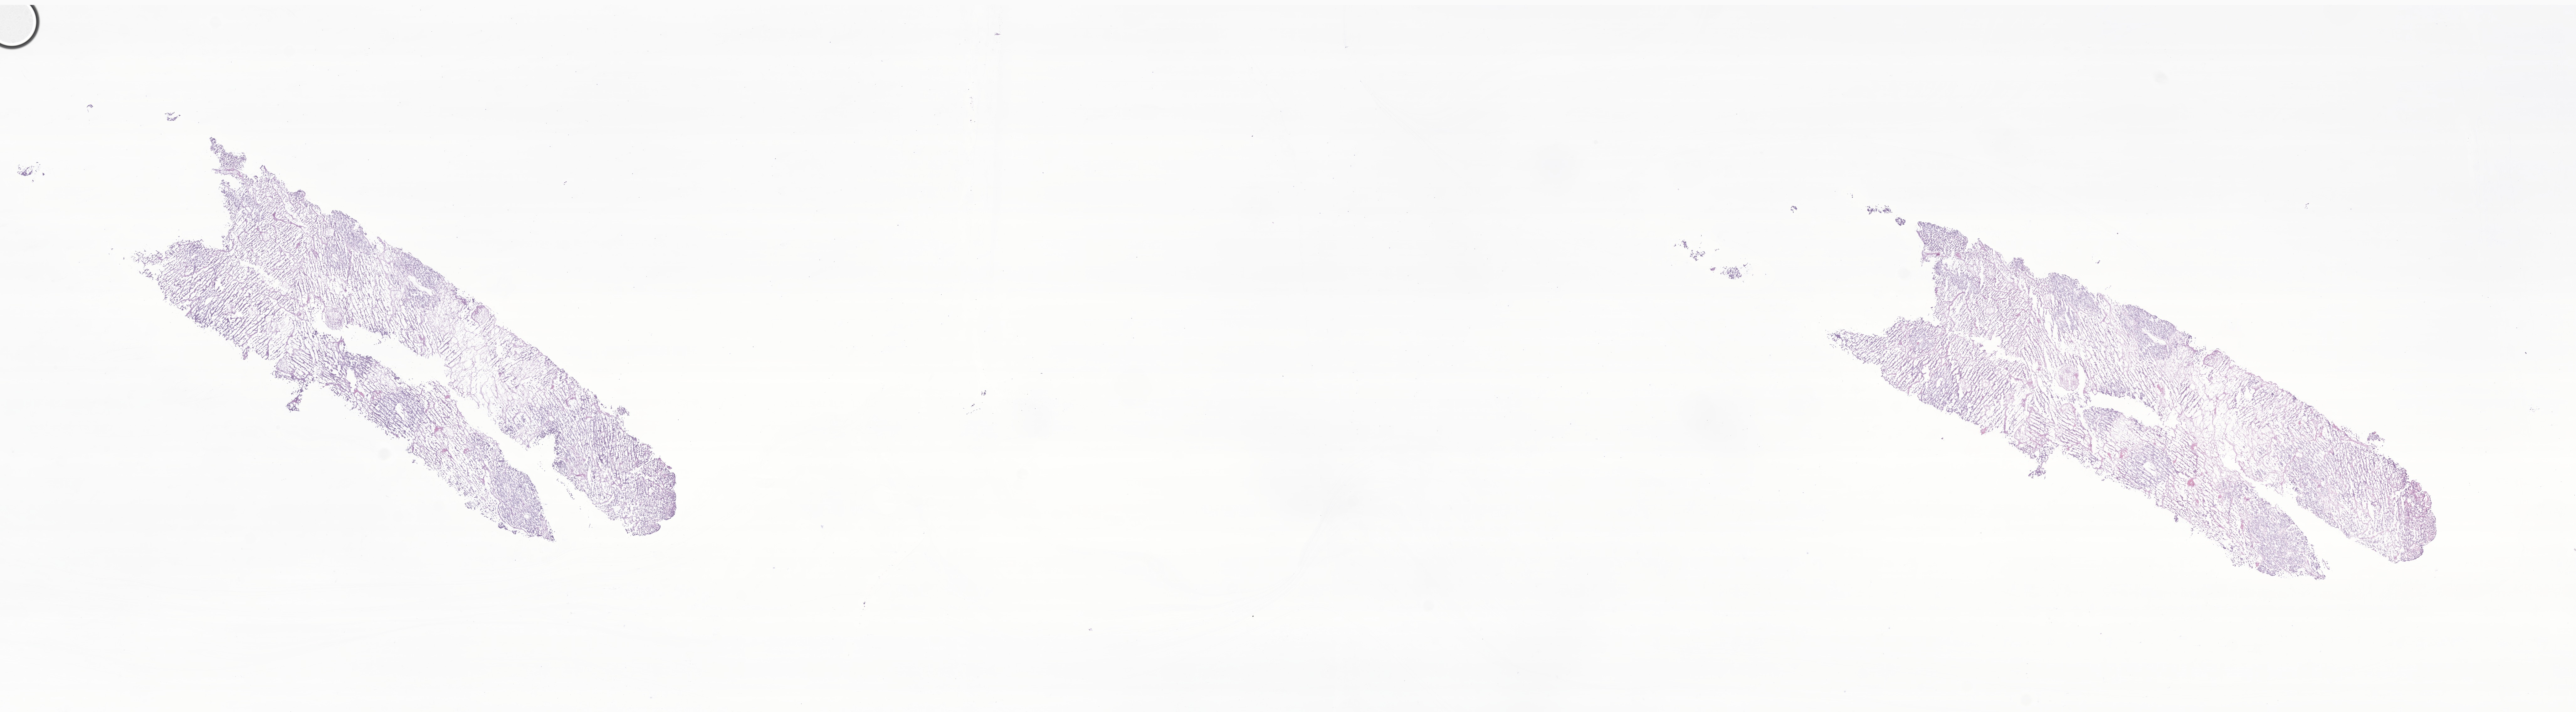
Hematoxylin and eosin (H&E) whole-slide image of tumor tissue from the brain, whole scanned area (about 34.6 x 9.6 mm) shown as a low-resolution overview. Cryosection (OCT / tissue freezing medium). Patient male; age 81 months (6 years 9 months).
Diagnosis (ICD-O-3 morphology term): Medulloblastoma, NOS.